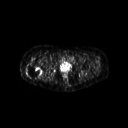
FDG PET of an extremity soft-tissue mass (from a PET/CT study), one axial slice; position 44 of 267 along the scan axis; 128 × 128 image matrix, field of view 600 × 600 mm. Female patient, age 57 years. From the clinical record (not read from this slice): histological type: epithelioid sarcoma with vascular differentiation; site of the primary tumour: right buttock.
Structures marked on this image (expert contour drawn on MRI and transferred to this co-registered scan by the dataset authors):
- gross tumour volume (mass): bounding box <24,62,43,80> (left, top, right, bottom; pixels)